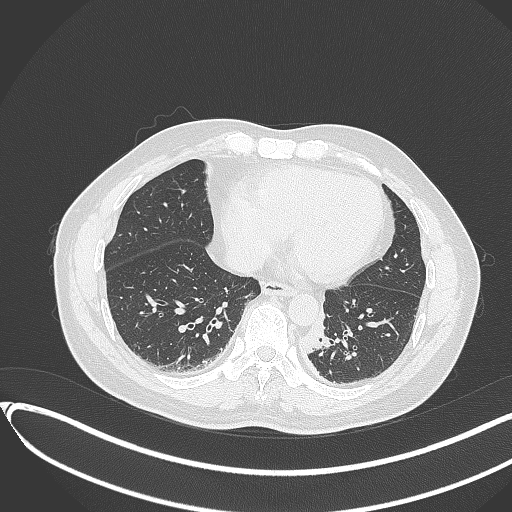
Chest CT, one axial slice; position 104 of 417 along the scan axis; reconstruction kernel B70f; lung window (W 1500 / L -600 HU); 1 mm slice thickness; 512 × 512 image matrix, field of view 400 × 400 mm. Male patient, age 54 years. From the clinical record (not read from this slice): clinical TNM (as recorded): T3 N0 M0.
Annotated regions visible in this slice (rectangle marked by the reading radiologist):
- lung tumour (recorded histology: squamous cell carcinoma): box from (x=298, y=293) to (x=333, y=357) px